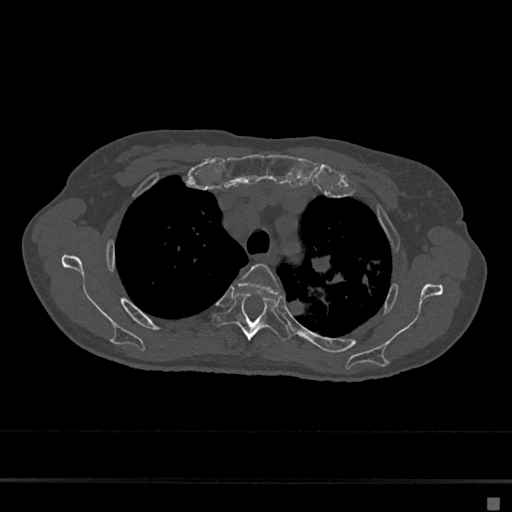
CT including the spine, one axial slice; position 513 of 797 along the scan axis; 120 kVp; bone window (W 1800 / L 400 HU); 0.5 mm slice thickness; 512 × 512 image matrix, field of view 360 × 360 mm. Female patient, age 68 years. Case-level facts recorded for this patient, not image findings: primary cancer: renal.
Structures marked on this image (semi-automatic segmentation, software-assisted and operator-edited):
- T3 vertebra: bounding box (x1, y1, x2, y2) in pixels: (237, 263, 280, 296)
- T4 vertebra: (212, 293, 291, 341)